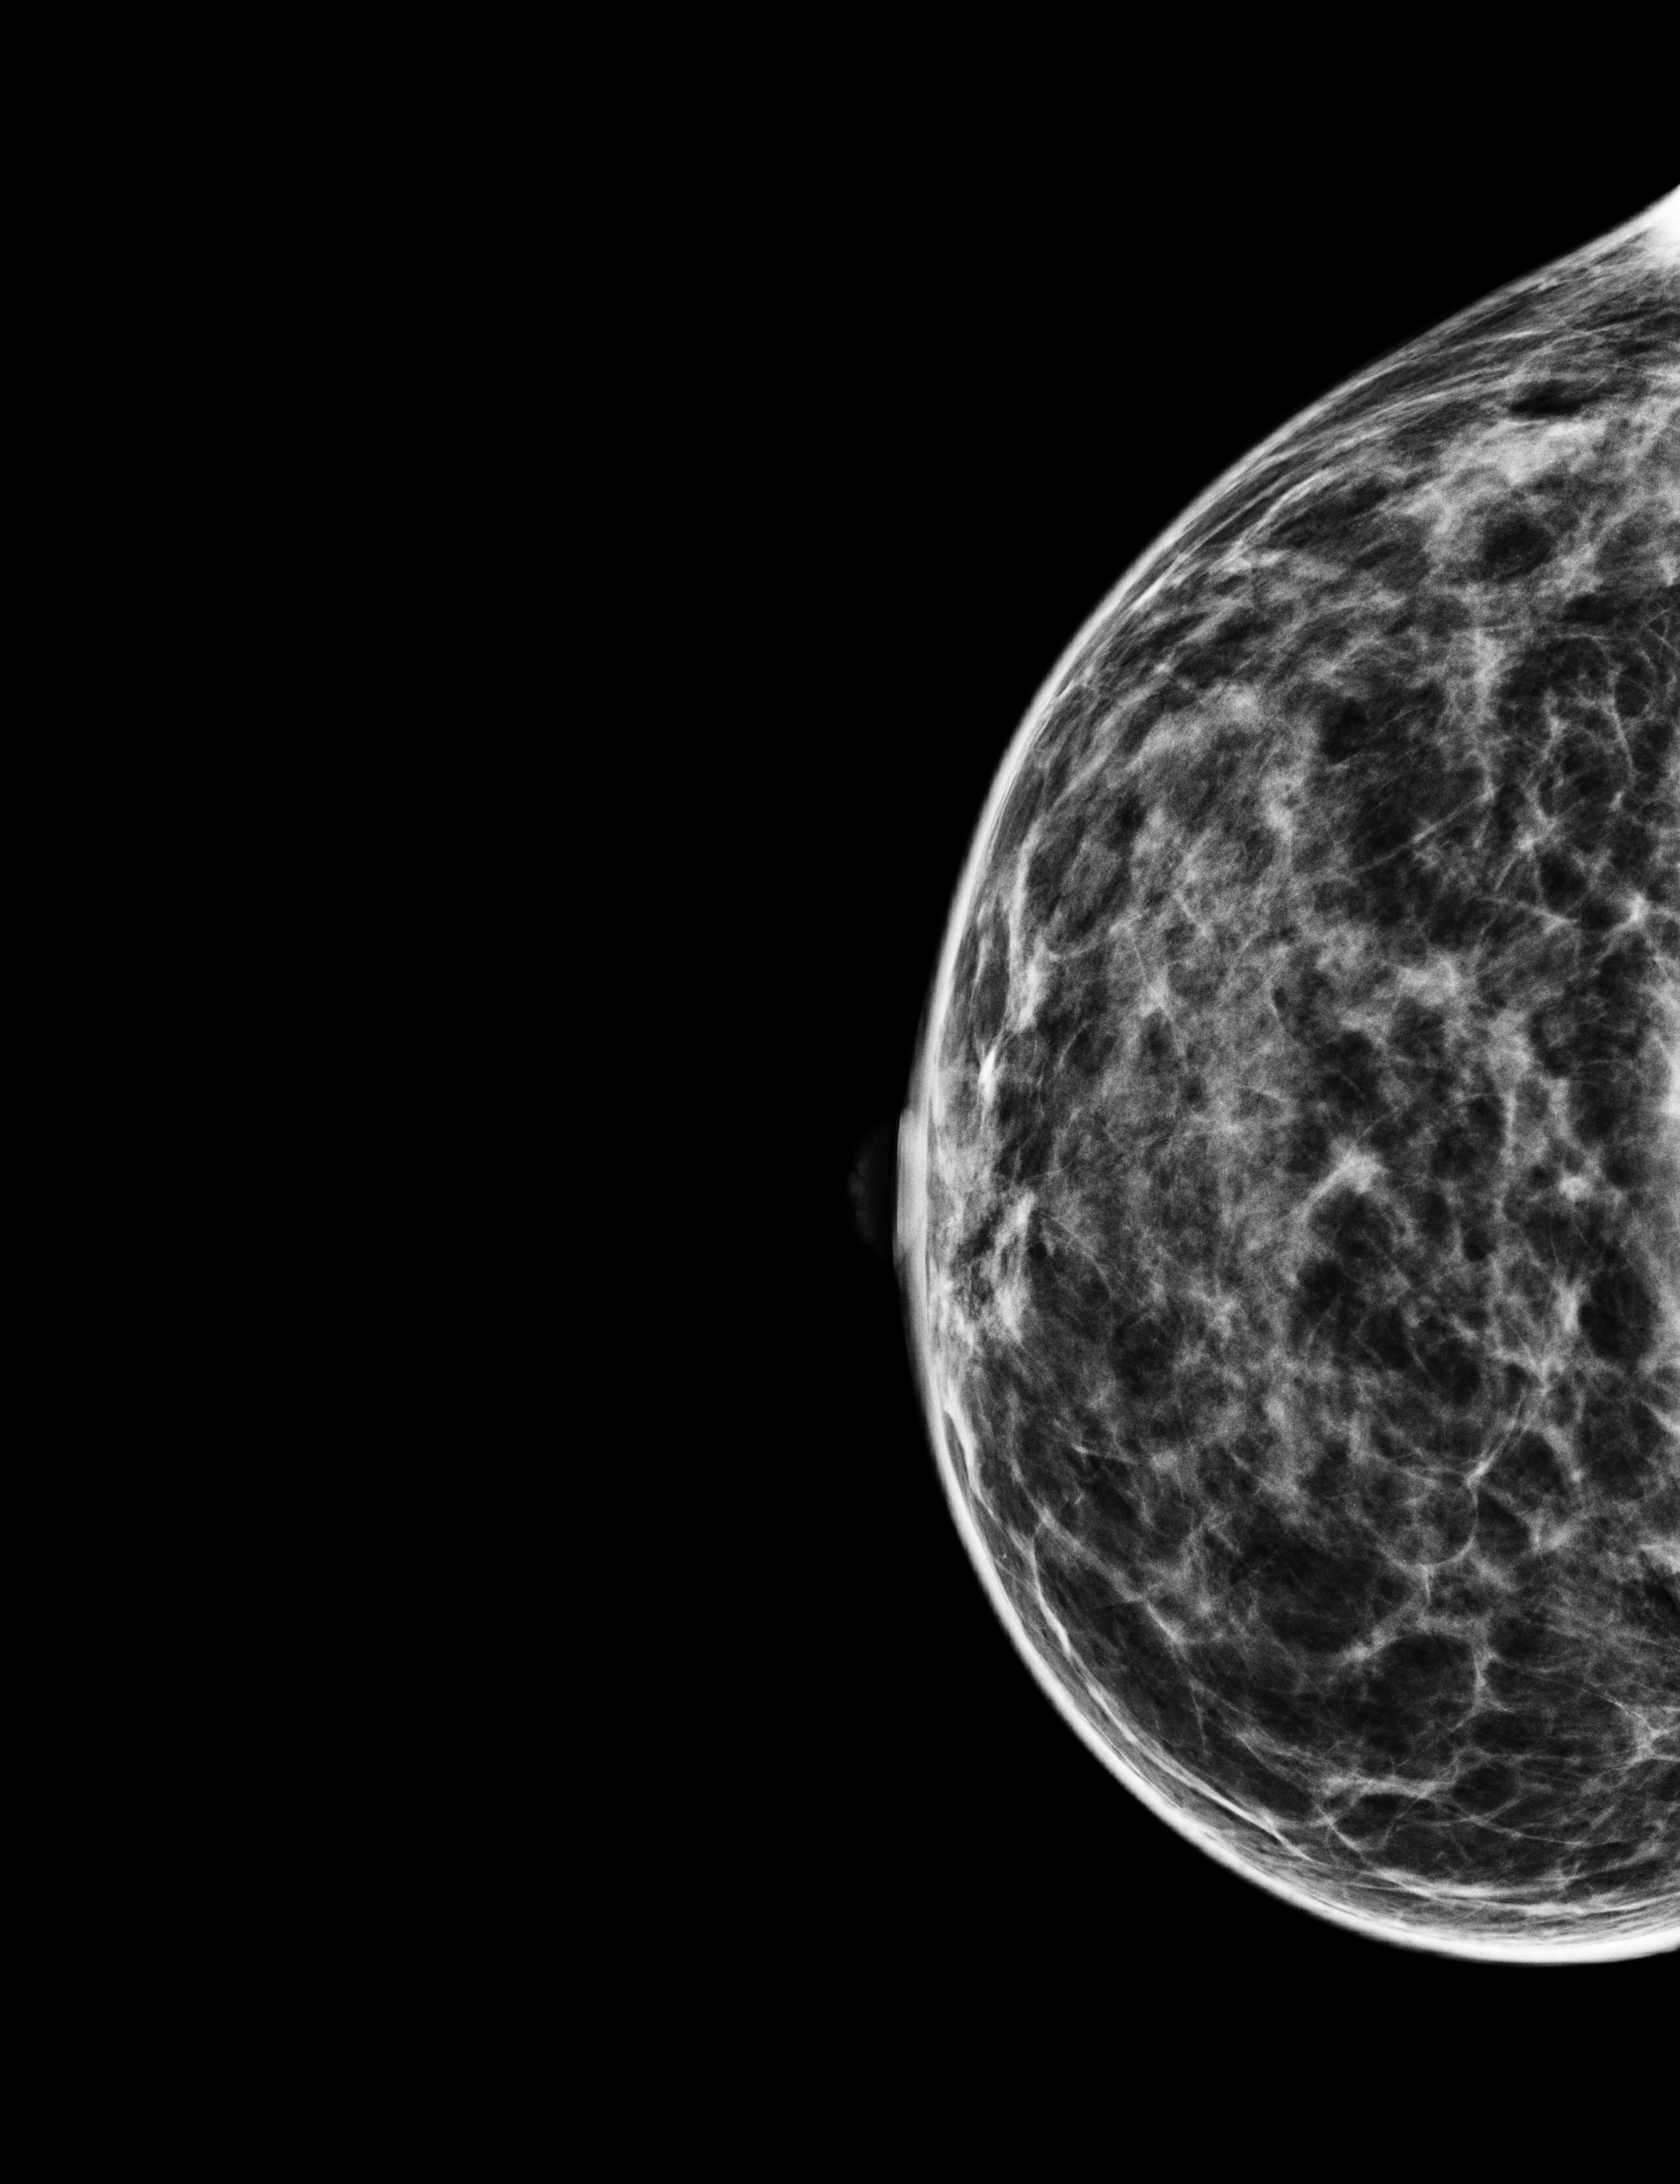
Full-field digital mammogram (FFDM); right breast; craniocaudal (CC) view; screening examination; compressed breast thickness 50 mm. Female patient, age 43 years.
- BI-RADS breast density category at the screening exam (both breasts, scale 1–4): 3
- final BI-RADS category for the screening round (tomosynthesis exam, both breasts): category 2
- recall: no recall after this screen